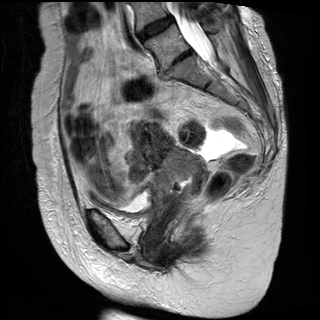
Pelvic MRI for cervical cancer, one sagittal slice; position 13 of 30 along the scan axis; T2-weighted; 1.5 T; TE 89 ms, TR 2930 ms; 320 × 320 image matrix. Patient: female, 61 years.
Structures marked on this image (manually delineated by an expert):
- uterus and cervix: bounding box (x1, y1, x2, y2) in pixels: (131, 120, 210, 218)